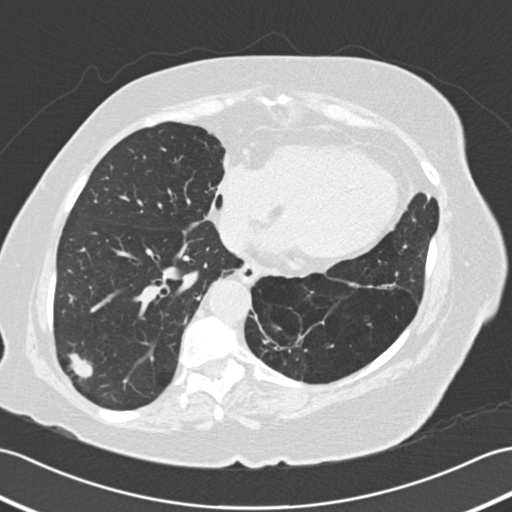
Low-dose screening chest CT, one axial slice. Lung window (W 1500 / L -600 HU). 2 mm slice thickness. 512 × 512 image matrix, field of view 353 × 353 mm.
Annotated regions visible in this slice (manually delineated by an expert):
- lesion 1 (tumor, lower lobe of right lung): bounding box [x1, y1, x2, y2] px = [69, 353, 93, 378]